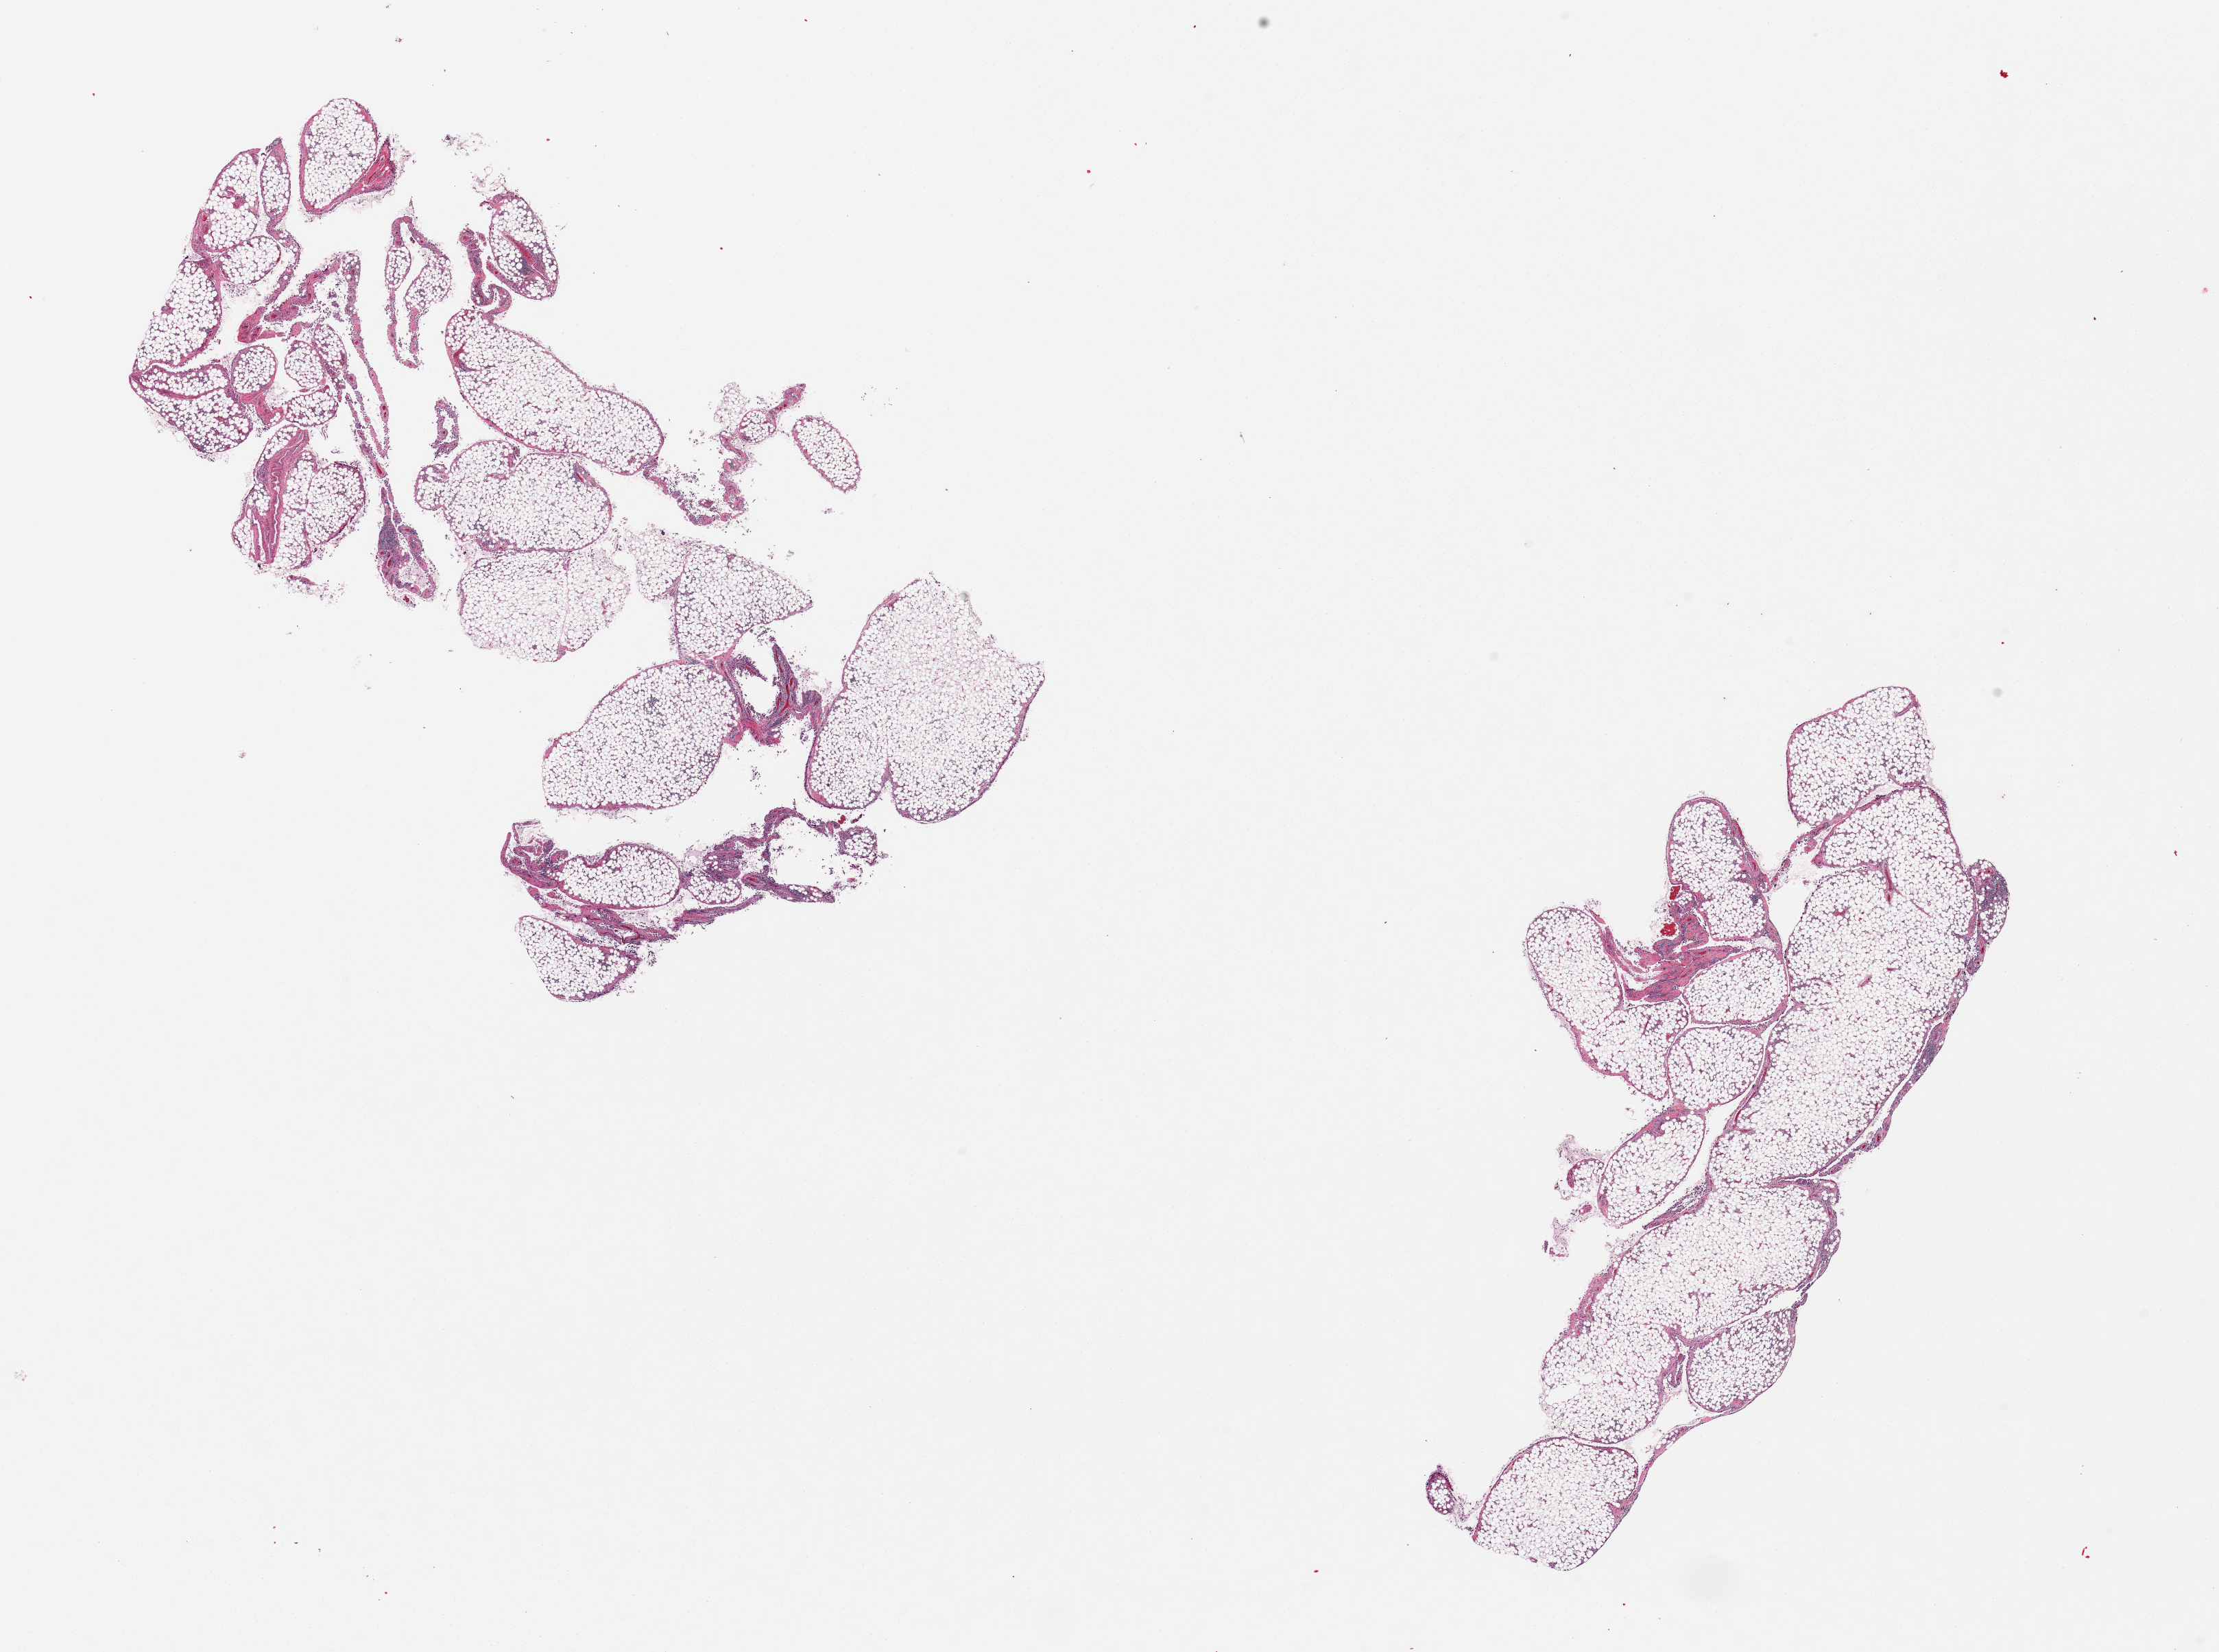
Whole-slide image, hematoxylin and eosin (H&E) stain — shown as a low-resolution overview of the whole scanned area (about 25.6 x 19.1 mm, acquisition: 20x scan), PAXgene-fixed, paraffin-embedded tissue, target tissue: omentum, donor tissue sample.
Reviewer comment on this tissue sample: 2 pieces.